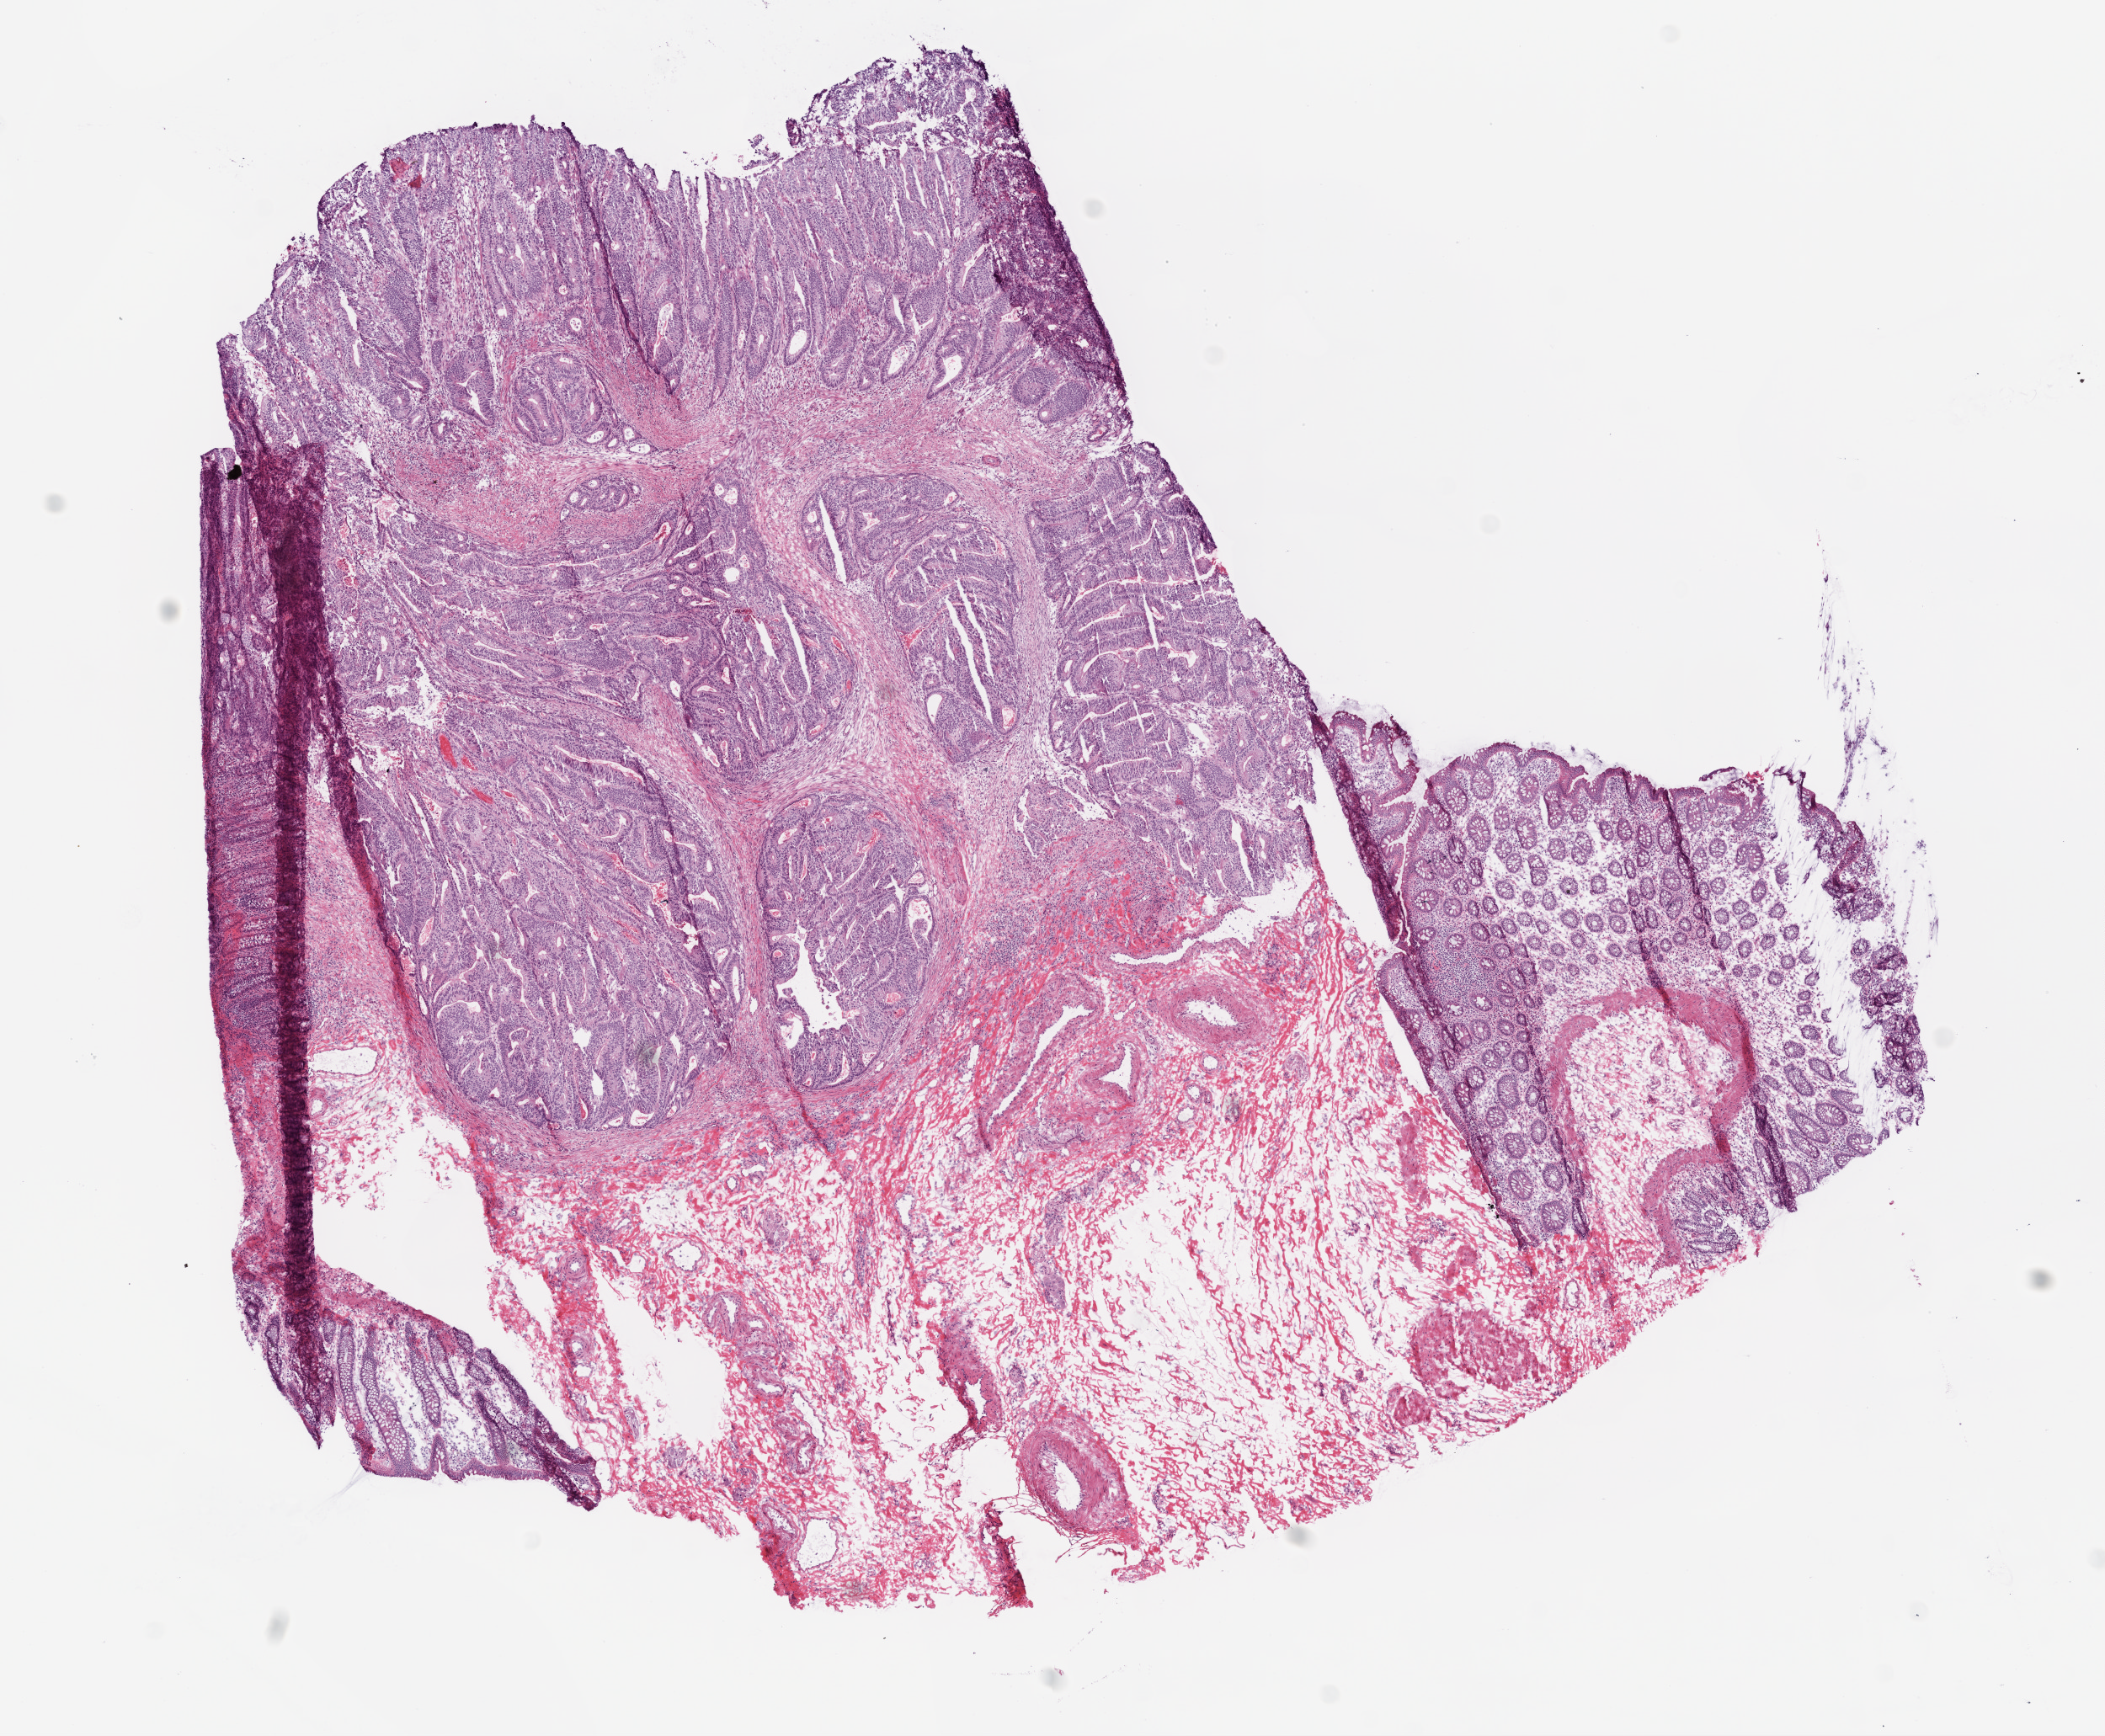
Whole-slide histology image, H&E — a low-resolution overview of the entire scanned area, about 10.0 x 8.3 mm (slide scanned at 20x), frozen section from the bottom of the tissue portion, primary tumour sample from the colon. Female, age 77 years at initial diagnosis. Slide review estimates, as recorded: tumour cells 70%, tumour nuclei 80%, normal cells 10%, stromal cells 20%, necrosis 0%.
AJCC pathologic stage: IIA (6th edition). Lymph nodes positive (case pathology): 0 of 36 examined. Diagnosis: Adenocarcinoma, NOS (ascending colon).